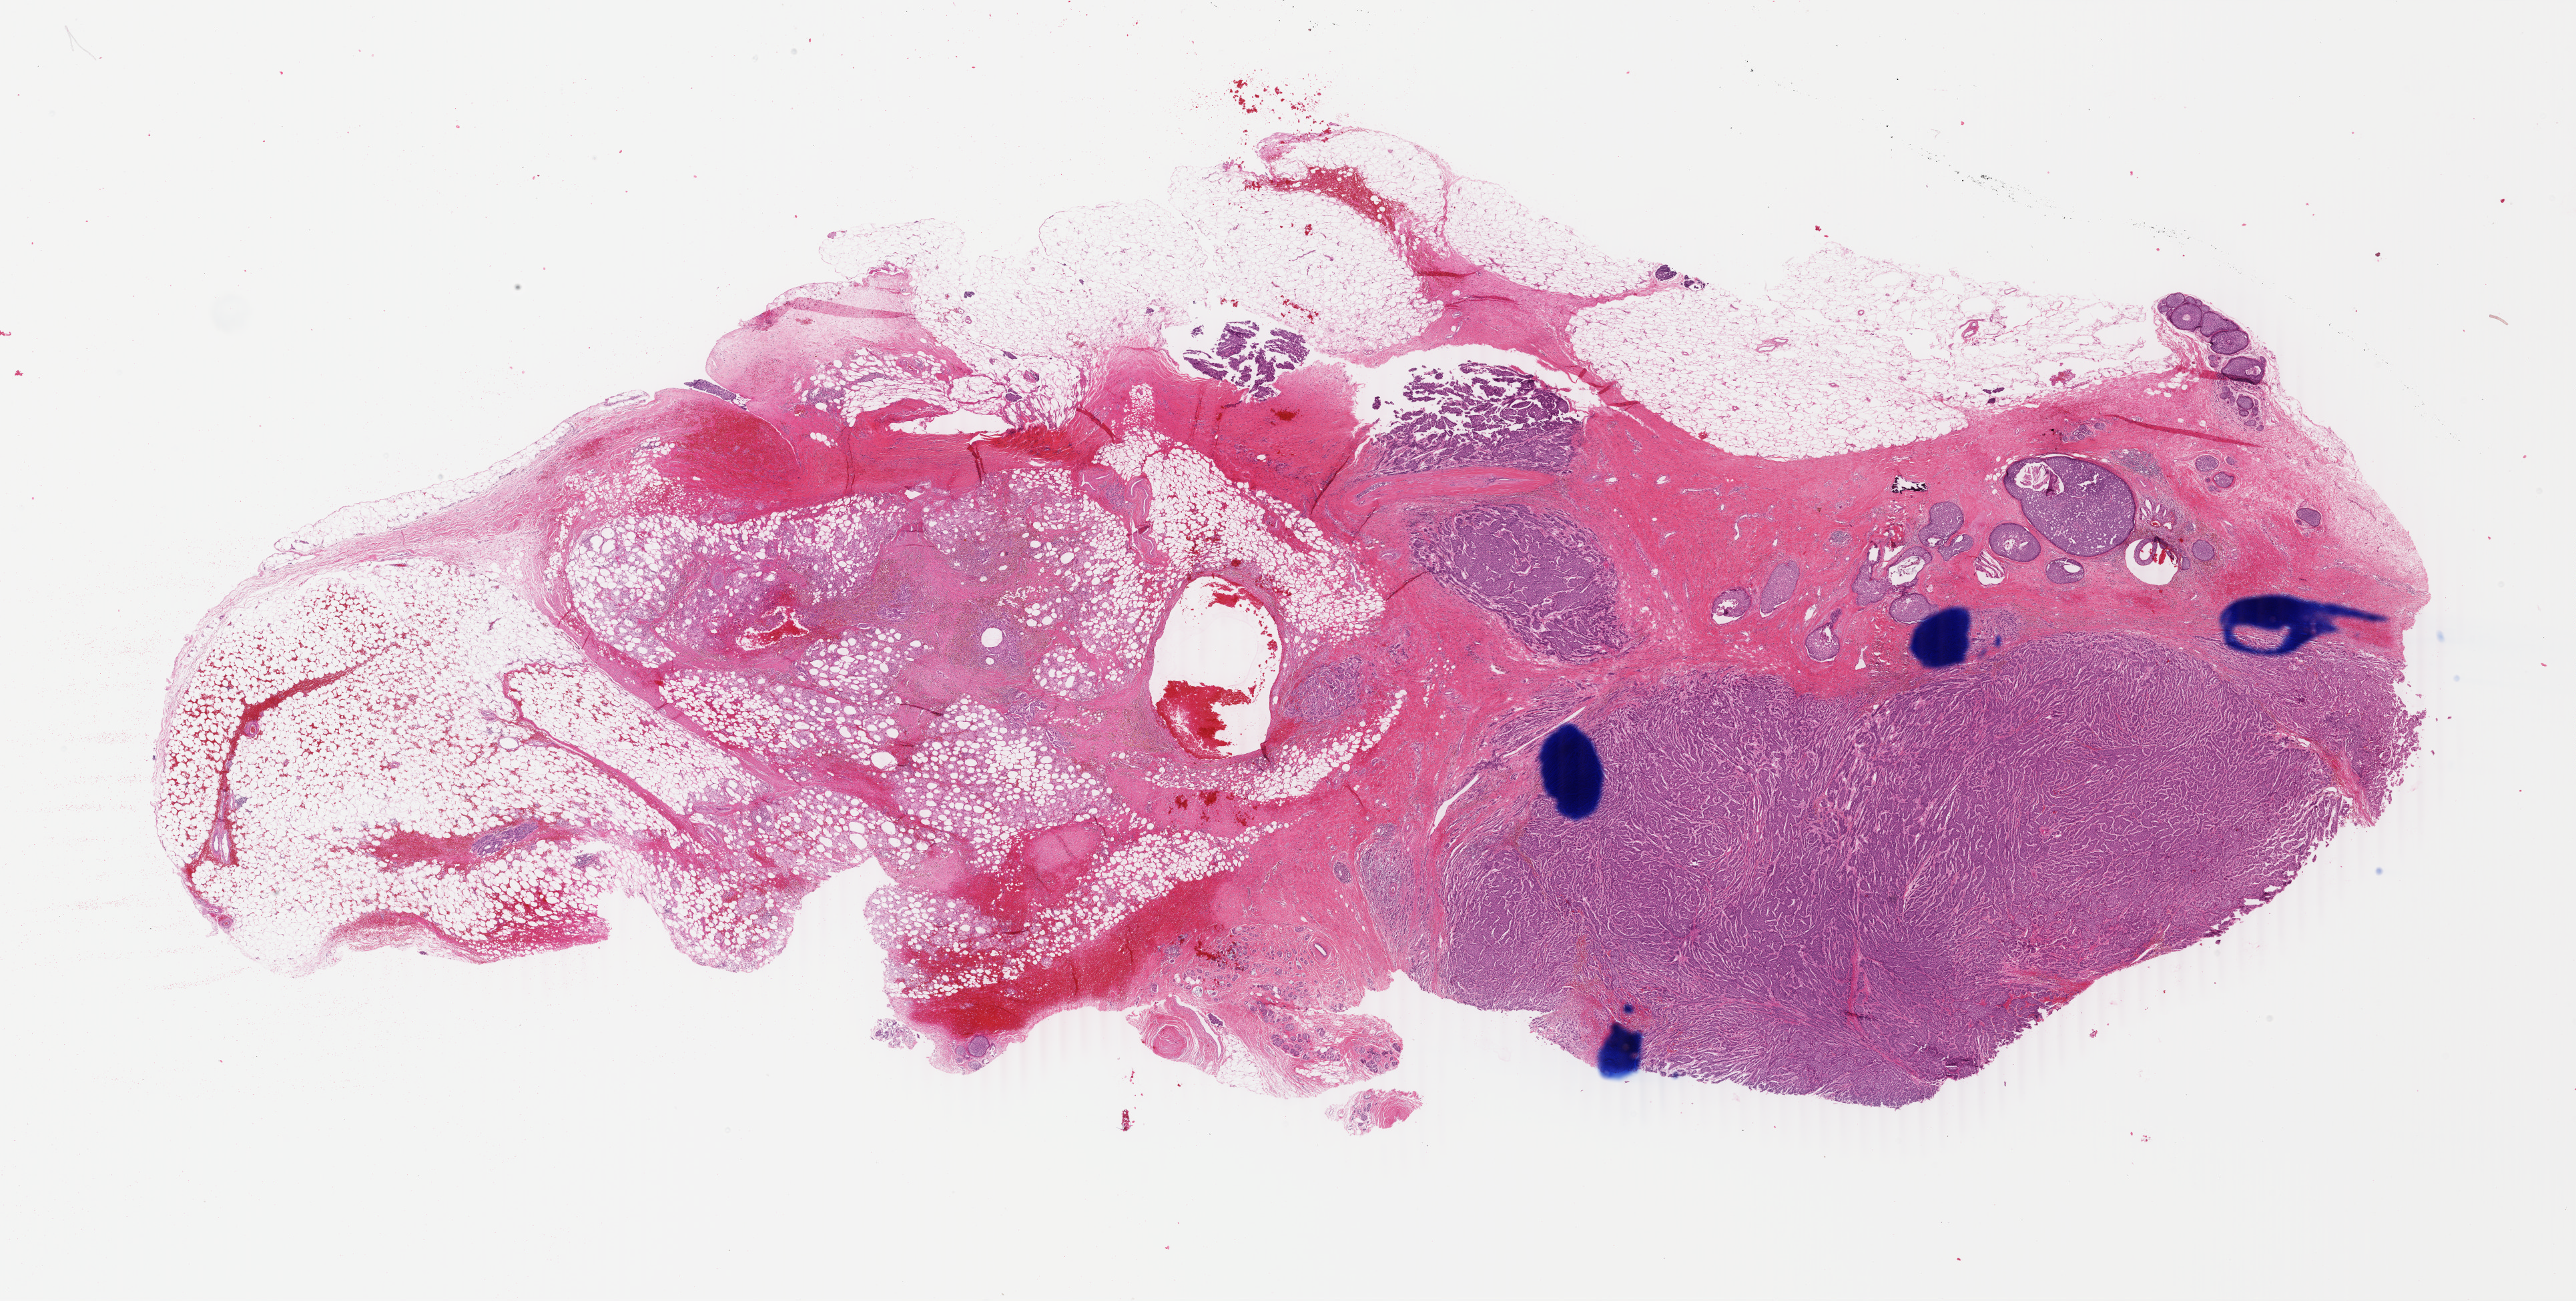
Digitized H&E-stained tissue section (whole slide) — shown as a low-resolution overview of the whole scanned area (about 30.7 x 15.5 mm); formalin-fixed paraffin-embedded (FFPE) diagnostic section; sample: primary tumour, breast. Female patient; age at initial diagnosis 61 years.
• pathologic diagnosis: Infiltrating duct carcinoma, NOS
• TNM: T2 N1b M0
• AJCC pathologic stage: IIB (4th edition)
• lymph nodes positive (case pathology): 3 of 14 examined